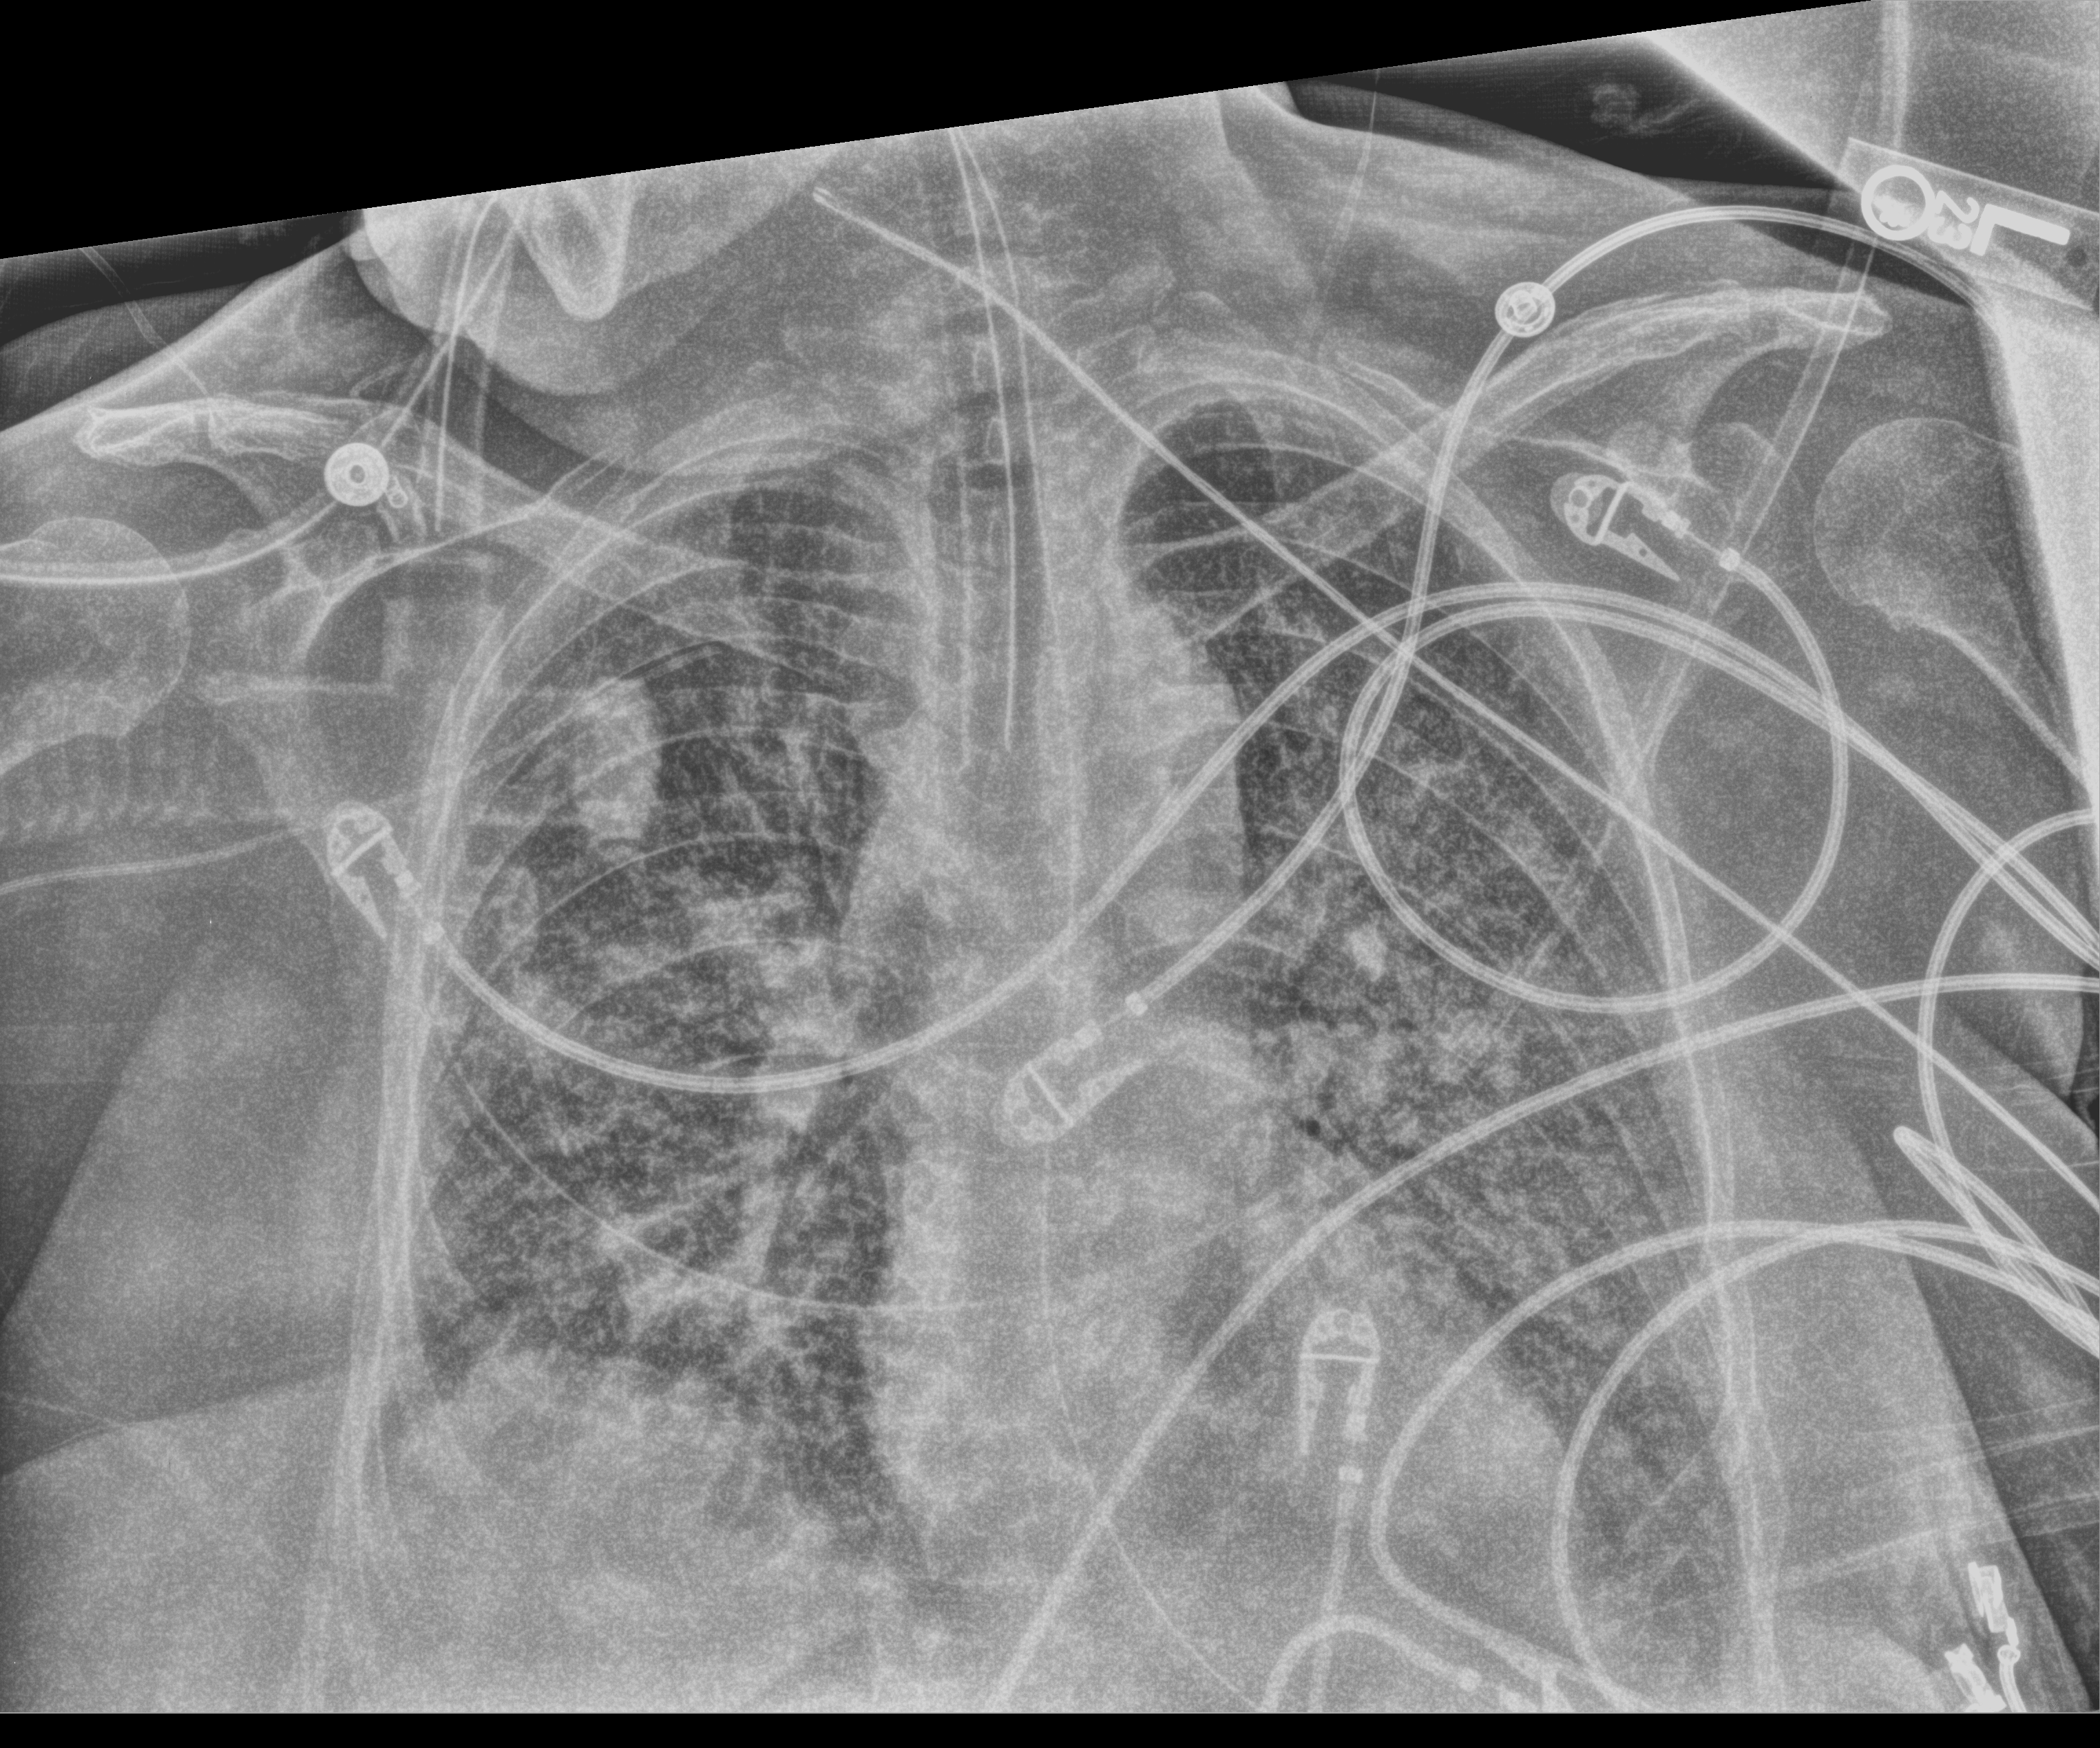
Portable chest radiograph, anteroposterior (AP) projection. Patient hospitalised with COVID-19; female, aged 60–74 years.
Admission-level facts for this patient (not findings on this image; timing relative to this image not recorded): diabetes (admission record): yes; admitted to intensive care during this hospital stay: yes; mechanically ventilated during this hospital stay: yes.